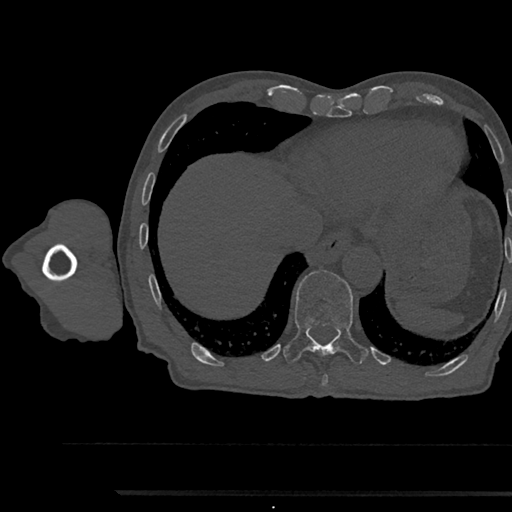
CT including the spine, one axial slice. Position 797 of 797 along the scan axis. Reconstruction kernel Br40s/3. 120 kVp. Bone window (W 1800 / L 400 HU). 0.5 mm slice thickness. 512 × 512 image matrix, field of view 367 × 367 mm. Patient: male, 79 years. From the clinical record (not read from this slice): primary cancer: prostate.
Structures marked on this image (semi-automatic segmentation, software-assisted and operator-edited):
- T11 vertebra: box from (x=283, y=272) to (x=368, y=360) px